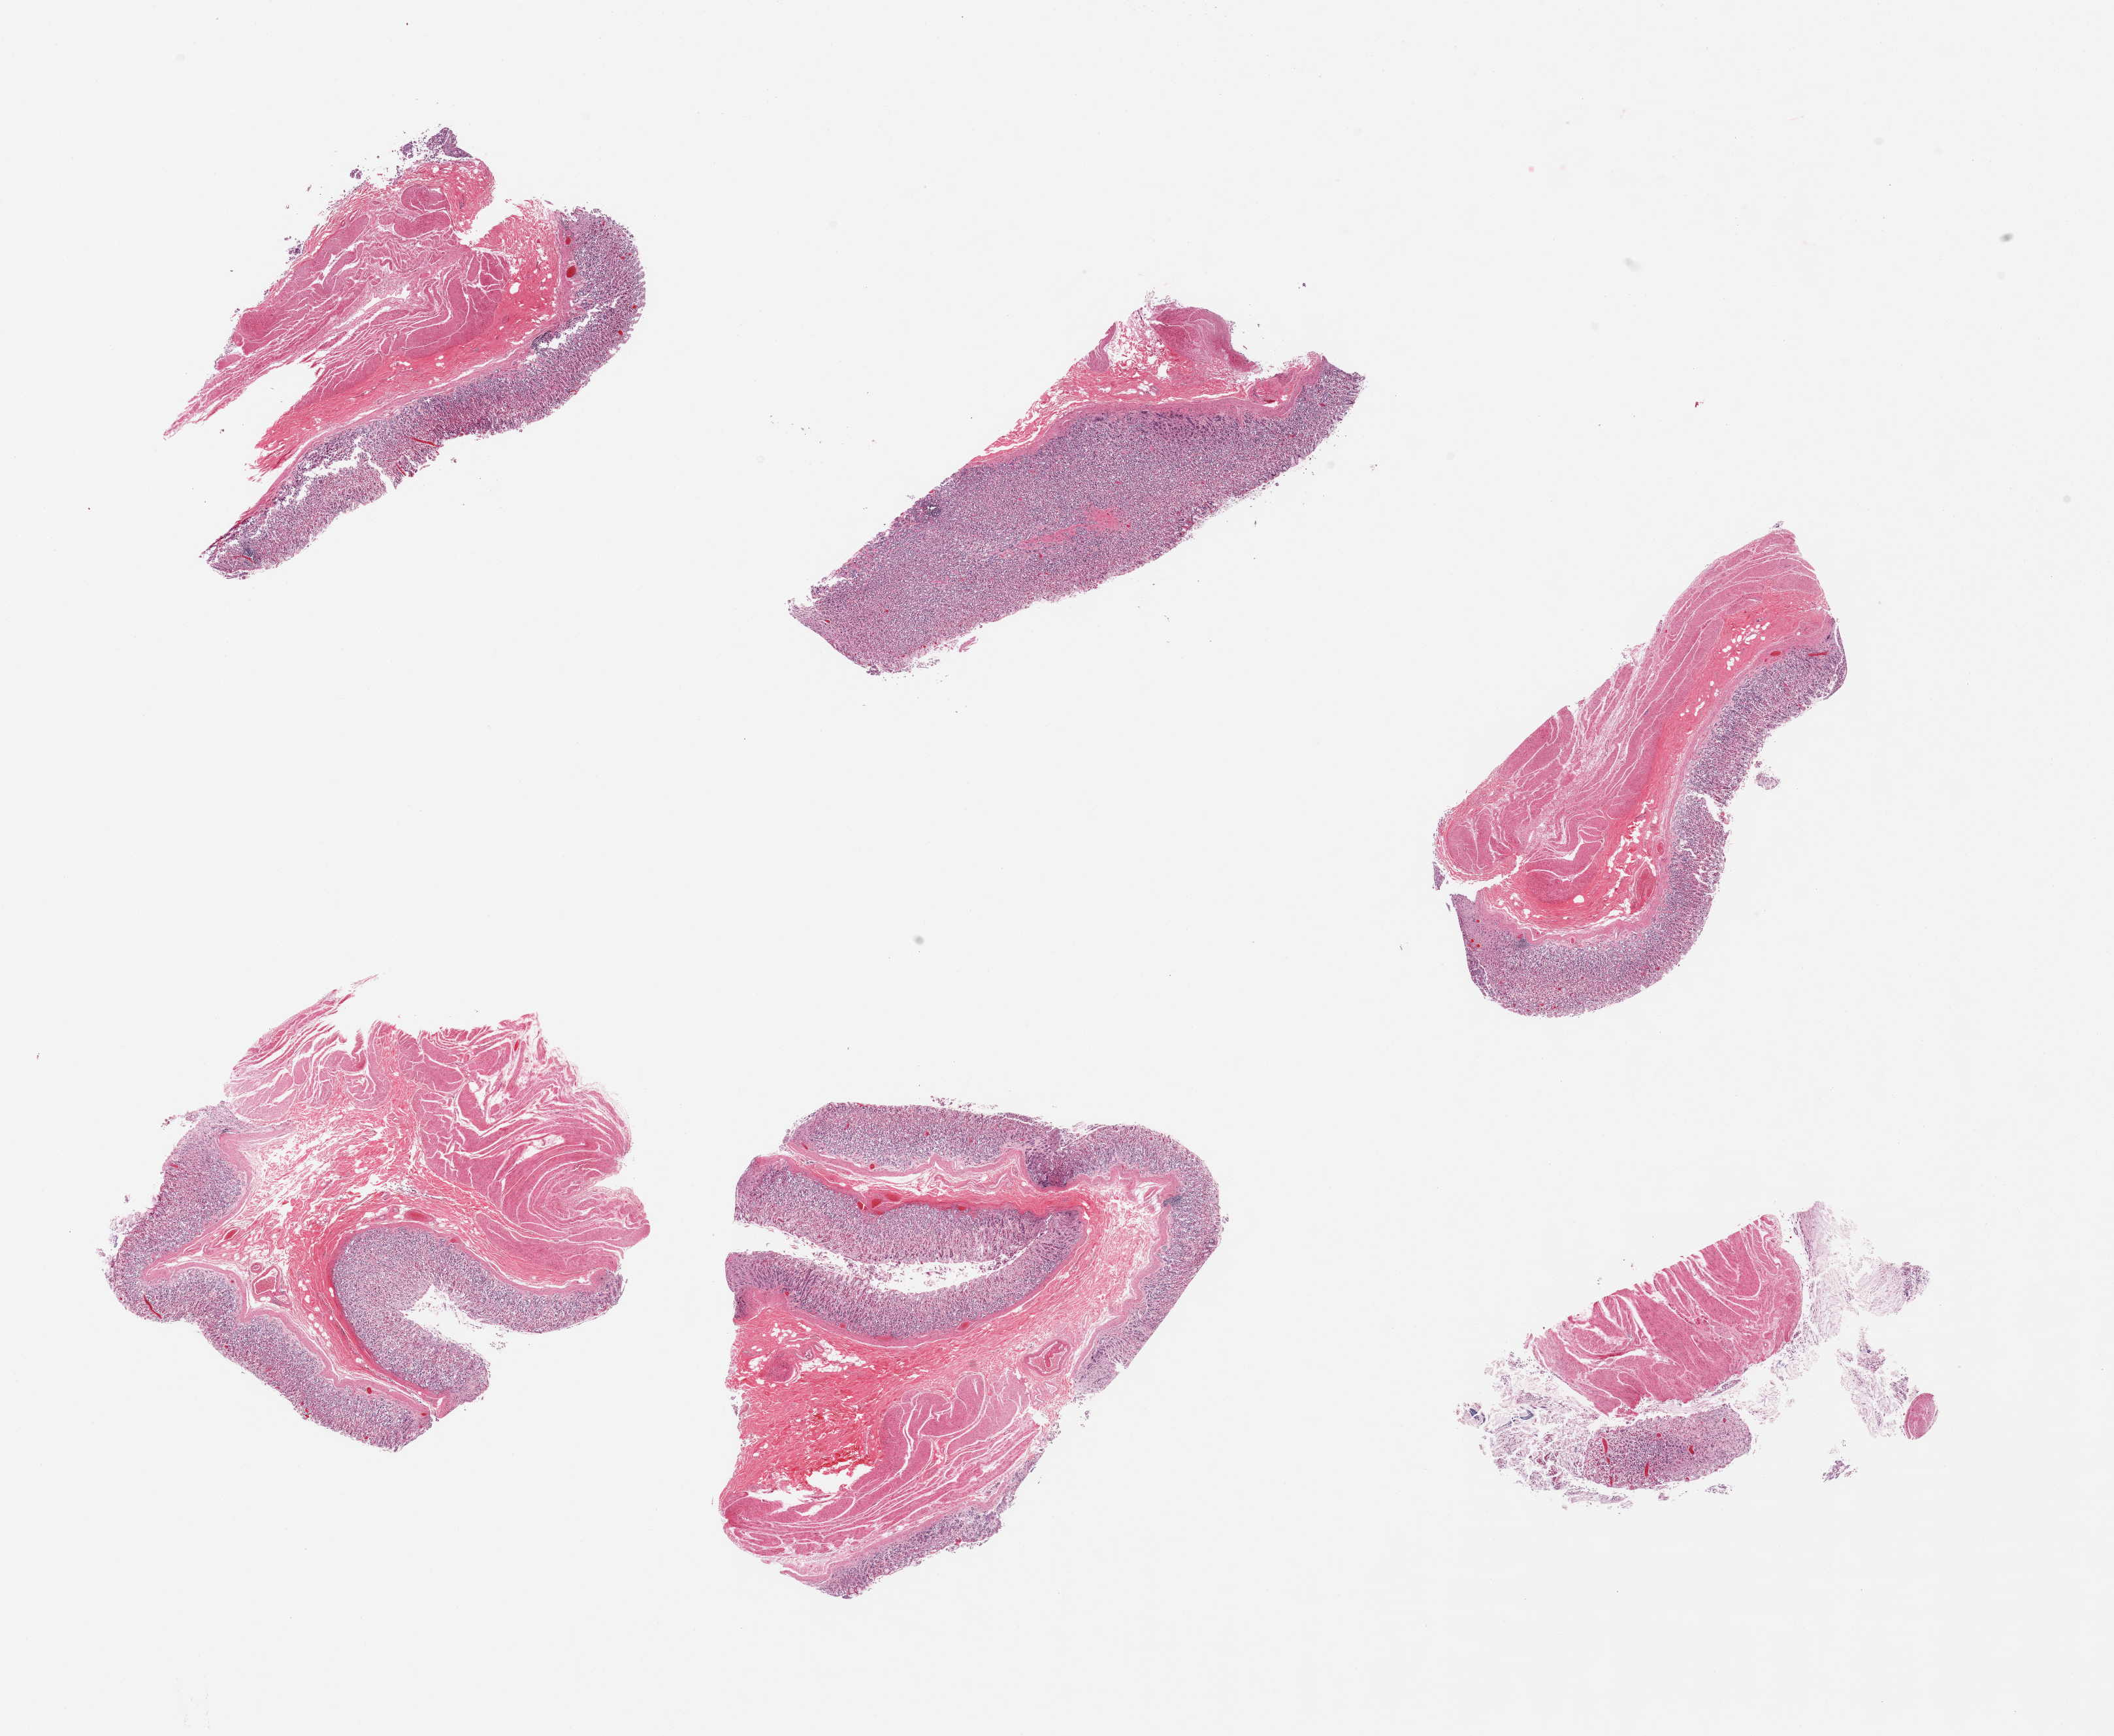
Whole-slide image, hematoxylin and eosin (H&E) stain, brightfield — whole scanned area (about 25.6 x 21.0 mm, slide scanned at 20x) shown as a low-resolution overview. PAXgene-fixed, paraffin-embedded tissue. Target tissue: stomach. Tissue donor sample. Donor: male.
Review note (as recorded): 6 pieces, mucosa up to ~1mm thick but moderately autolyzed.